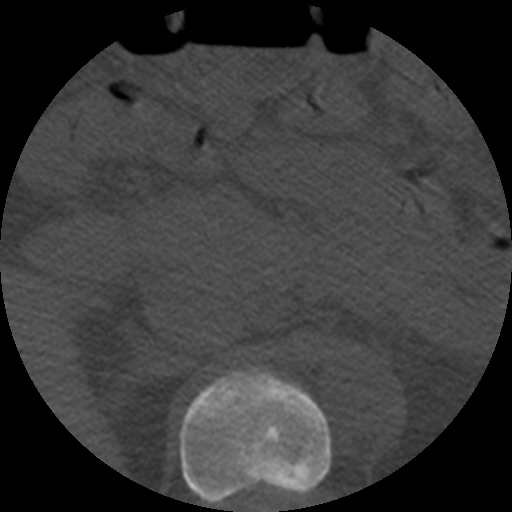
CT including the spine, one axial slice. Slice 233 of 508 in the series (ordered by position). Reconstruction kernel STANDARD. Bone window (W 1800 / L 400 HU). 1.25 mm slice thickness. 512 × 512 image matrix, field of view 160 × 160 mm. Patient age 57 years. Case-level facts recorded for this patient, not image findings: primary cancer: prostate.
Annotated regions visible in this slice (semi-automatic segmentation, software-assisted and operator-edited):
- T11 vertebra: box from (x=180, y=367) to (x=332, y=505) px